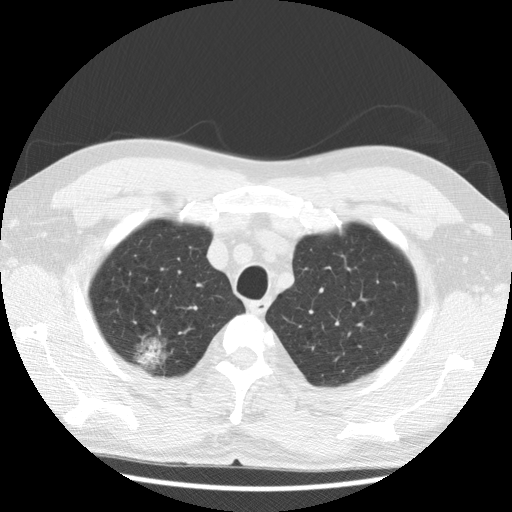
Low-dose screening chest CT, axial slice. Baseline annual screen. Lung window (W 1500 / L -600 HU). 2.5 mm slice thickness. Slice 23 of 122 in the series. Male participant, aged 59 years at enrolment. Former smoker at enrolment.
Expert-annotated lung lesion, box from (x=123, y=328) to (x=180, y=383) px. Screening reader's record for this exam (one nodule recorded; not confirmed to be the boxed lesion): non-calcified nodule or mass ≥4 mm, right upper lobe, 30 × 28 mm, poorly defined margins, ground glass attenuation. Official screen result: positive, change unspecified: nodule(s) >= 4 mm or enlarging nodule(s), mass(es), or other non-specific abnormalities suspicious for lung cancer.